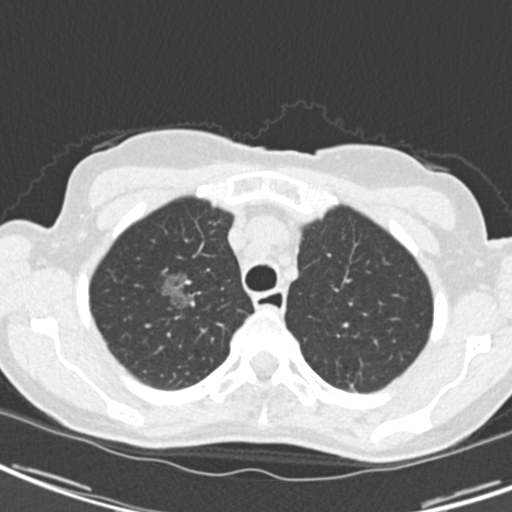
Low-dose screening chest CT, one axial slice. Position 161 of 189 along the scan axis. Lung window (W 1500 / L -600 HU). 2 mm slice thickness. 512 × 512 image matrix, field of view 279 × 279 mm.
Structures marked on this image (outlined manually by an expert reader):
- lesion 1 (tumor, upper lobe of right lung): bounding box <159,271,189,310> (left, top, right, bottom; pixels)